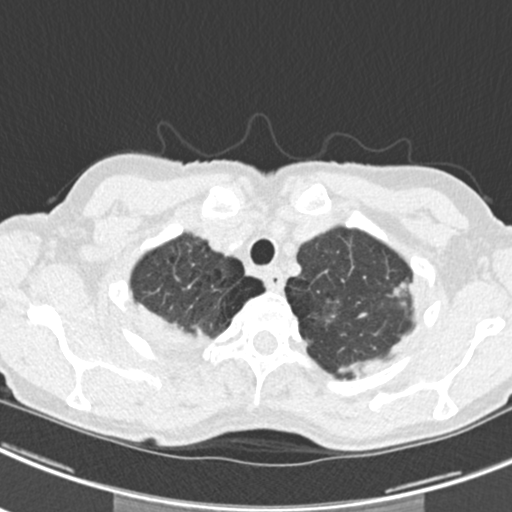
Chest CT (low-dose screening protocol), one axial image. Second annual screen. Lung window (W 1500 / L -600 HU). 2 mm slice thickness. 120 kVp. Slice 31 of 219 in the series. 512 × 512 image matrix. Female participant, aged 63 years at enrolment. Current smoker at enrolment.
Lesion marked by an expert reader, bounding box <363,261,425,321> (left, top, right, bottom; pixels). The screening reader recorded 9 non-calcified nodules or masses ≥4 mm on this exam (left upper lobe, right upper lobe, left upper lobe, left lower lobe, right middle lobe, left lower lobe, left lower lobe, right lower lobe, right lower lobe); which of them this box marks is not recorded. Official screen result: positive, other. Later outcome: lung cancer diagnosed 408 days after this screen — bronchiolo-alveolar adenocarcinoma, NOS, right upper lobe, right middle lobe, right lower lobe, left upper lobe, left lower lobe, moderately differentiated (G2), stage IV (AJCC 6th edition).